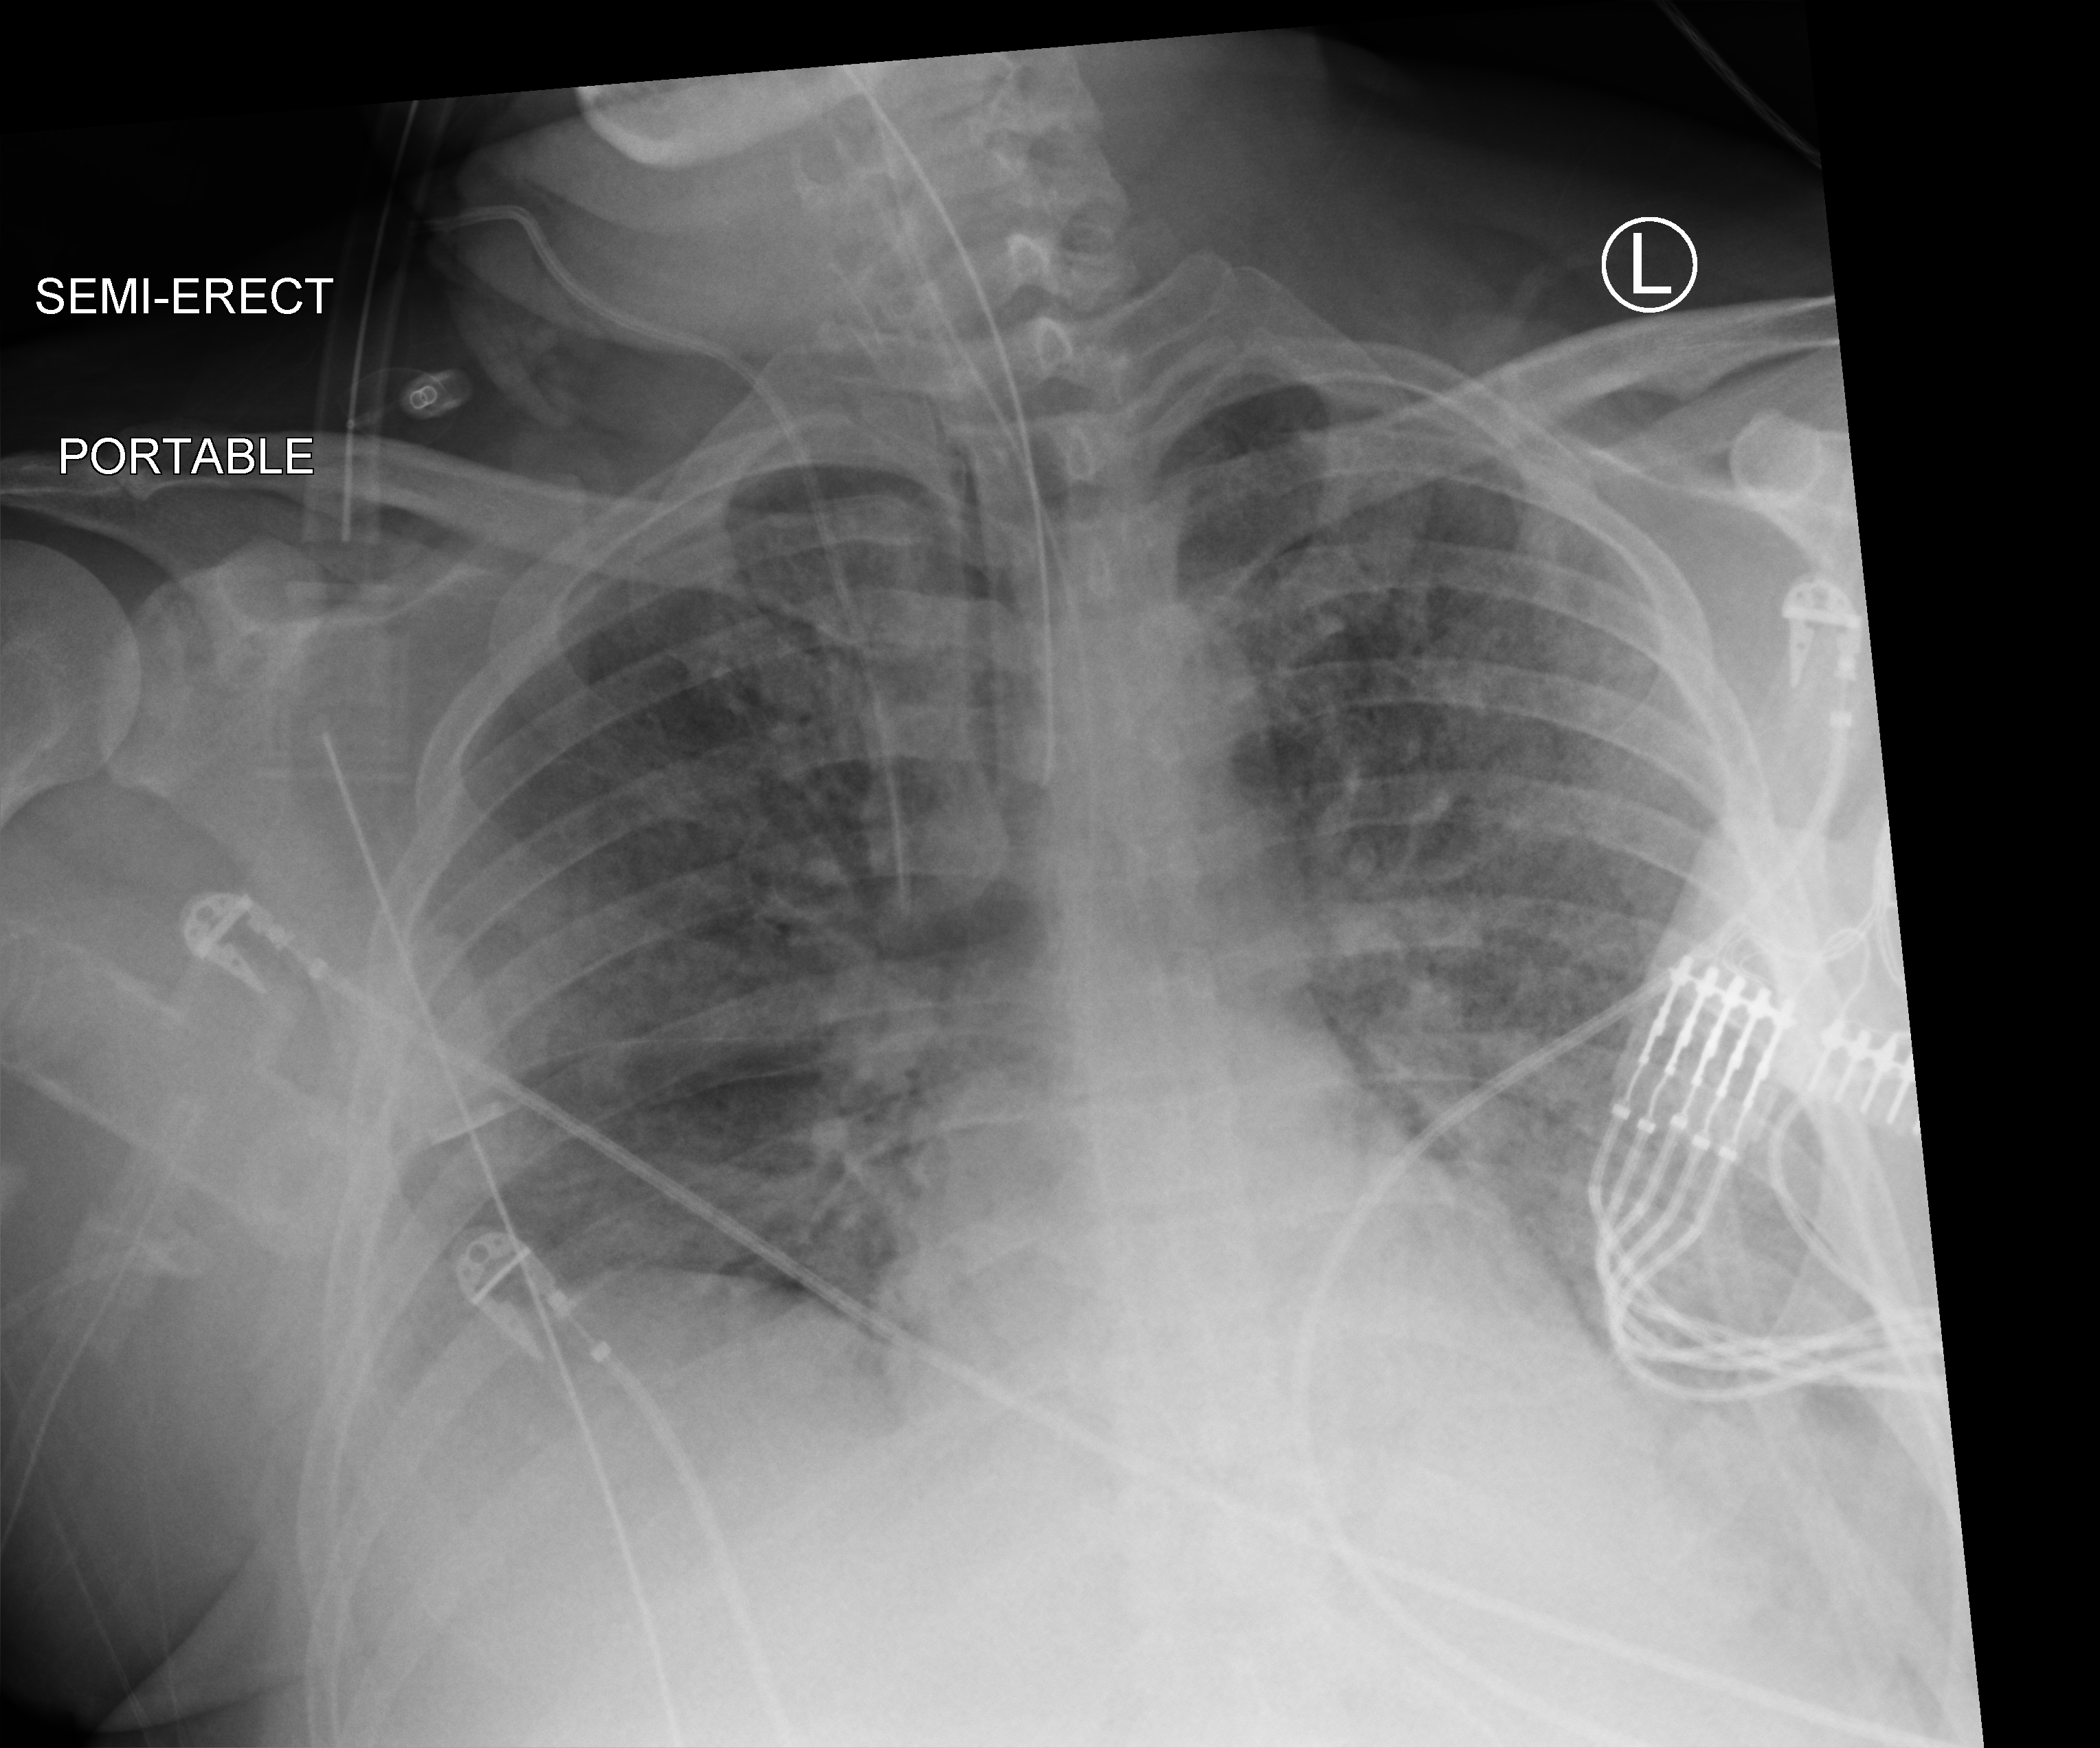
Bedside chest radiograph (computed radiography); anteroposterior (AP) projection. Patient hospitalised with COVID-19; male, aged 18–59 years.
Hospital-stay facts (about this admission, not read from this image; timing relative to this image not recorded): admitted to intensive care during this hospital stay: yes; mechanically ventilated during this hospital stay: yes.